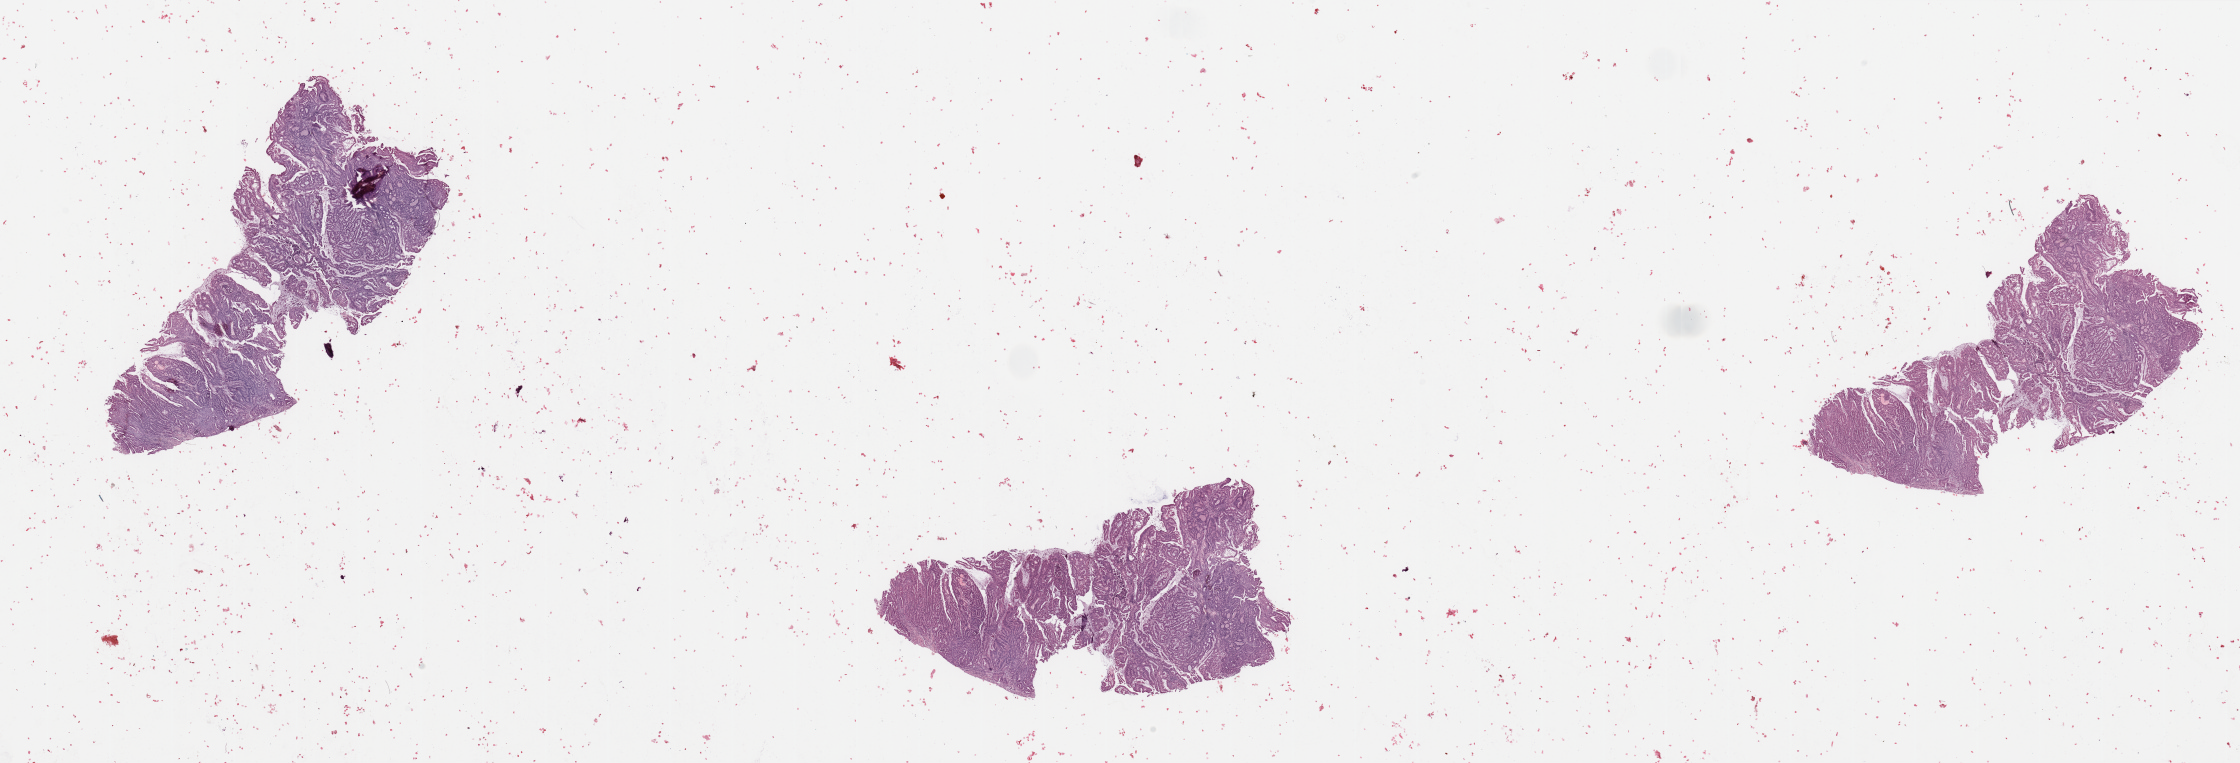
Digitized H&E tissue section (whole slide), low-resolution overview of the scanned area, about 35.4 x 12.1 mm (from a 20x scan), tumour tissue sample, sampled site: uterus. Patient: female, age 60 years. Histologic grade: G2 (moderately differentiated). Pathologist review of this section (percent, as recorded): tumour nuclei 90%, necrosis 2%.
AJCC pathologic stage: IV. Histologic diagnosis: Endometrioid adenocarcinoma, NOS.